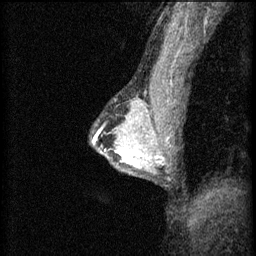
Breast MRI (dynamic contrast-enhanced), one sagittal slice. Position 41 of 60 along the scan axis. 3 images stored at this slice position (order not interpretable as contrast timing). 1.5 T. TE 4.2 ms, TR 8.2 ms. 2 mm slice thickness. 256 × 256 image matrix. Patient: female, 44 years.
Annotated regions visible in this slice (semi-automatically segmented with operator editing):
- analysis volume of interest (the breast-tissue region the enhancement analysis was run in; not a lesion): box from (x=102, y=132) to (x=151, y=169) px
- tumour enhancement mask (voxels above the 70 % enhancement threshold inside the analysis volume of interest): (x=104, y=136)–(x=151, y=165)